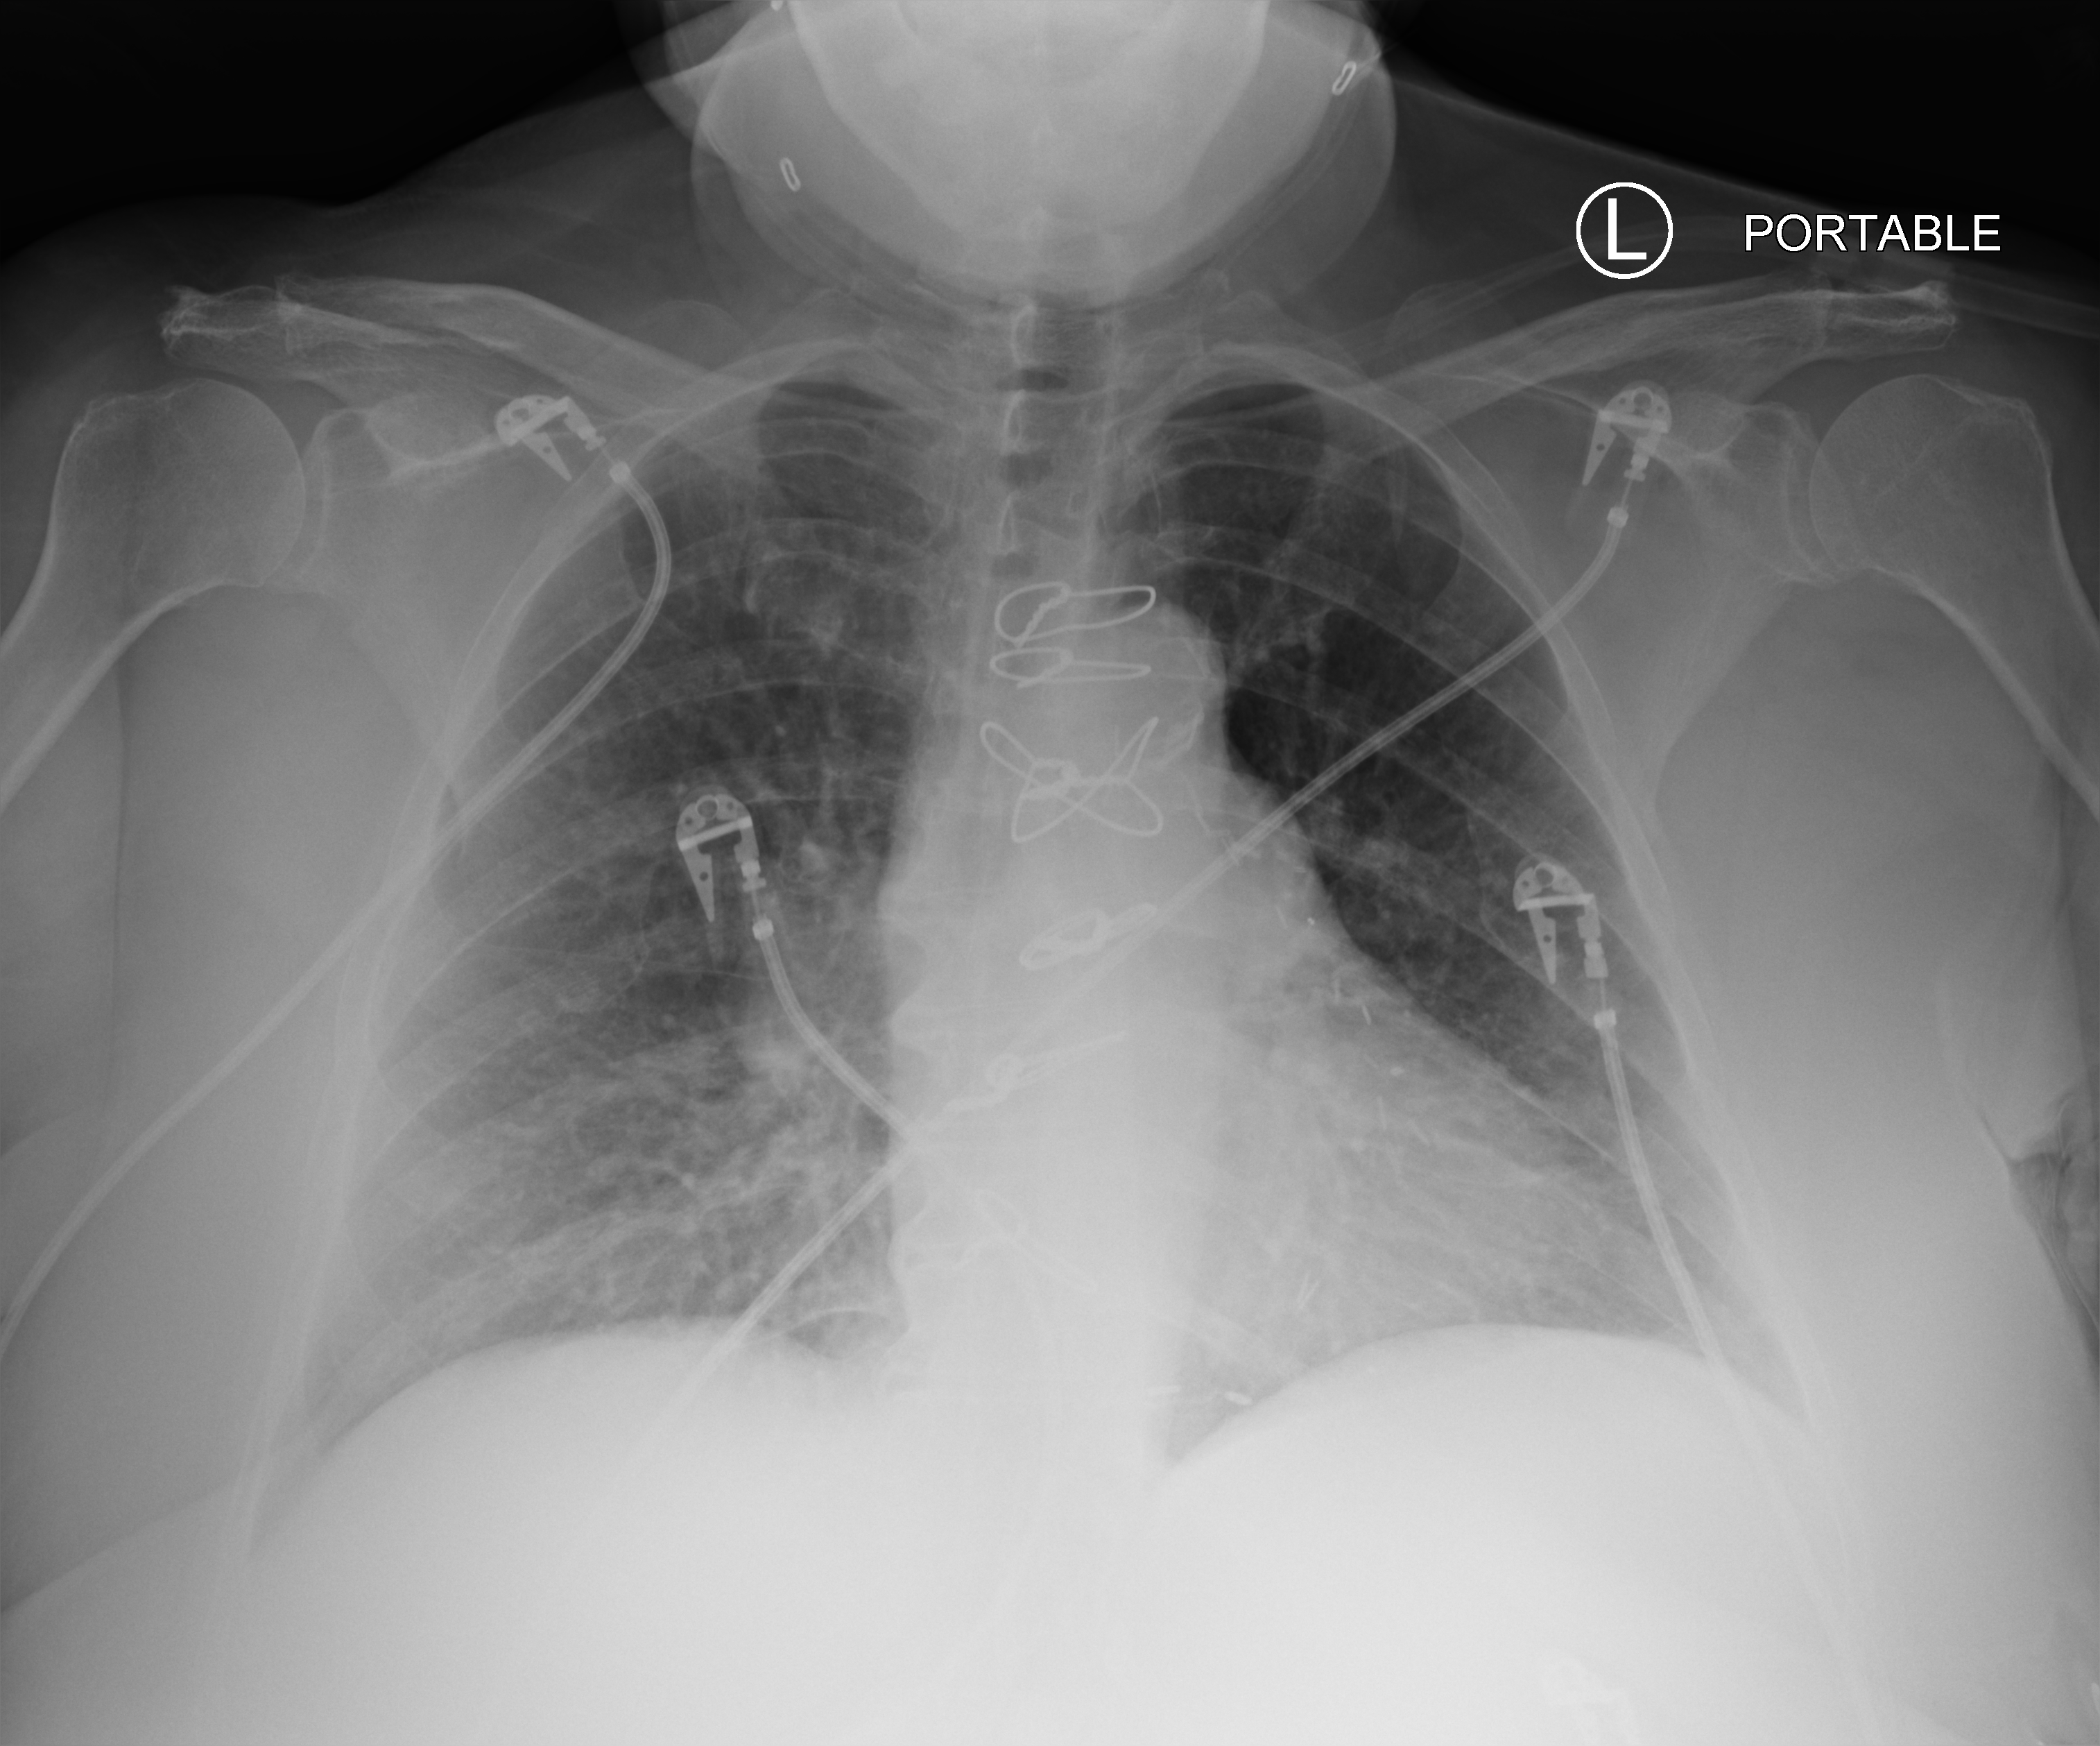
Chest X-ray (portable); anteroposterior (AP) projection. Patient hospitalised with COVID-19; female, aged 60–74 years.
From the hospital-stay record, not from the radiograph (when in the stay this image was taken is not recorded): admitted to intensive care during this hospital stay: no.